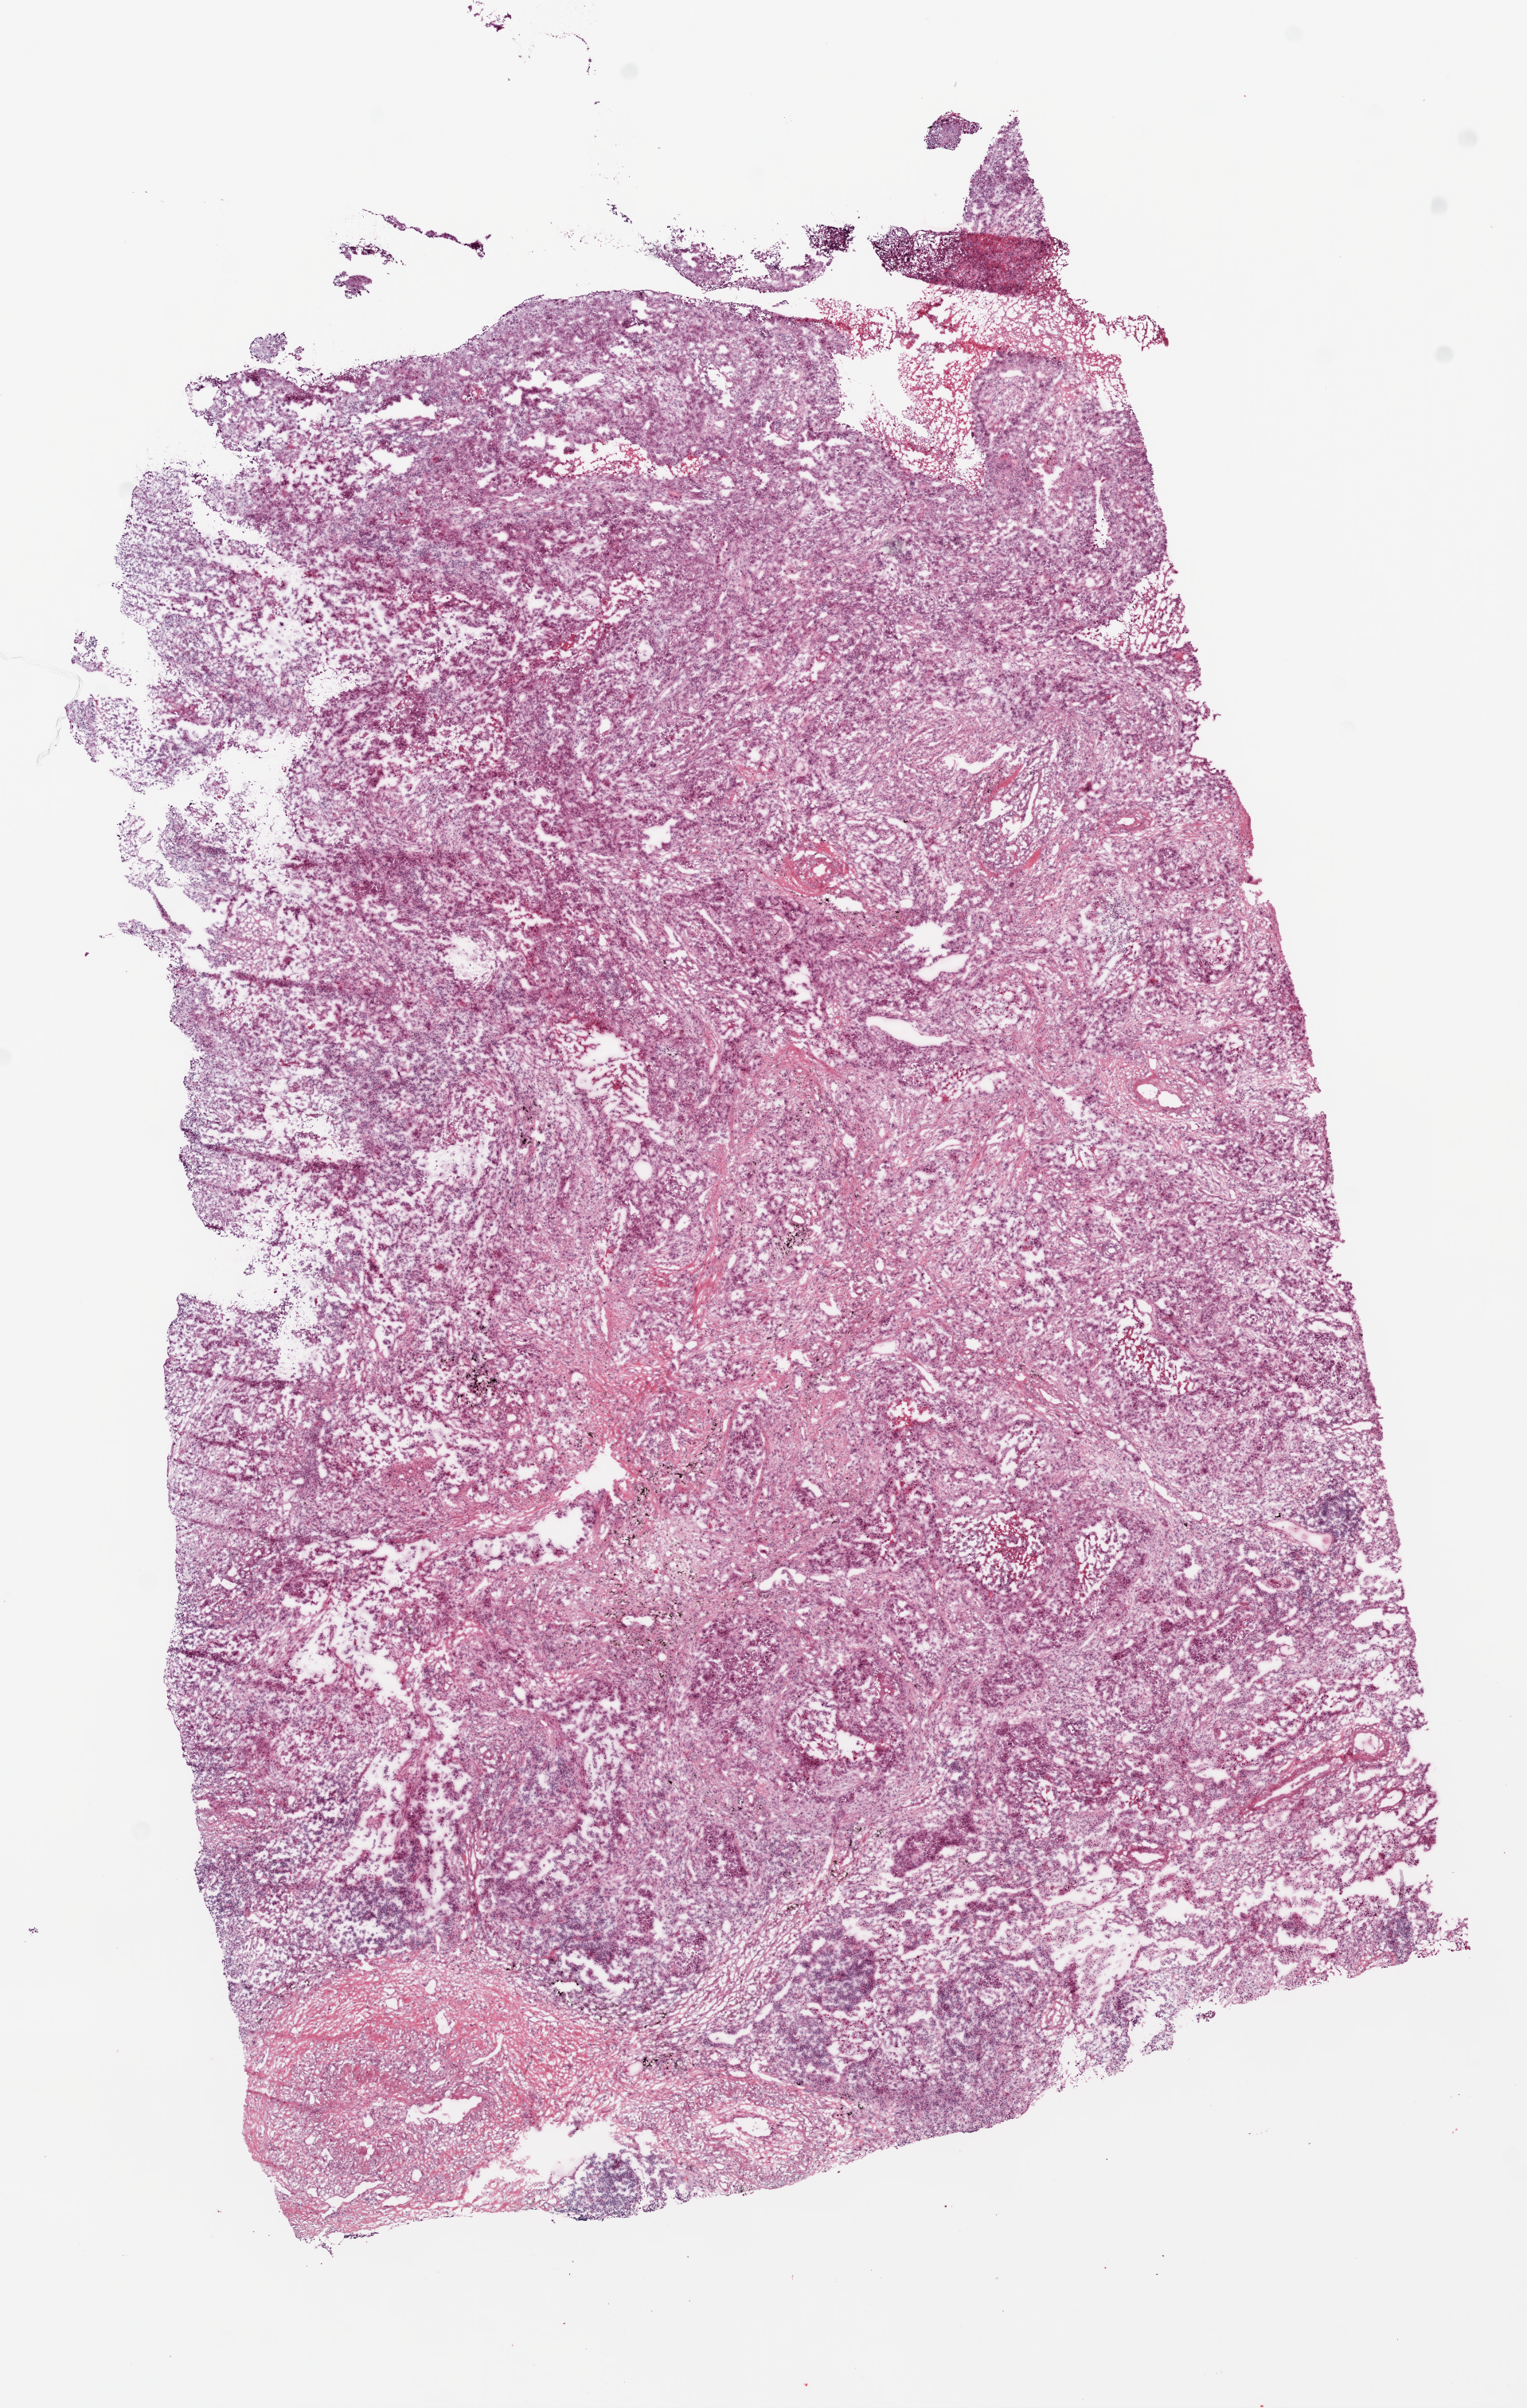
H&E-stained whole-slide image, low-resolution overview of the scanned area, about 7.7 x 12.2 mm (slide scanned at 20x); frozen section from the top of the tissue portion; lung, primary tumour sample. Female patient; age at initial diagnosis 80 years. Composition of this section per pathologist review: tumour nuclei 70%, necrosis 0%.
- AJCC pathologic stage: IB
- laterality: right
- diagnosis: Squamous cell carcinoma, NOS